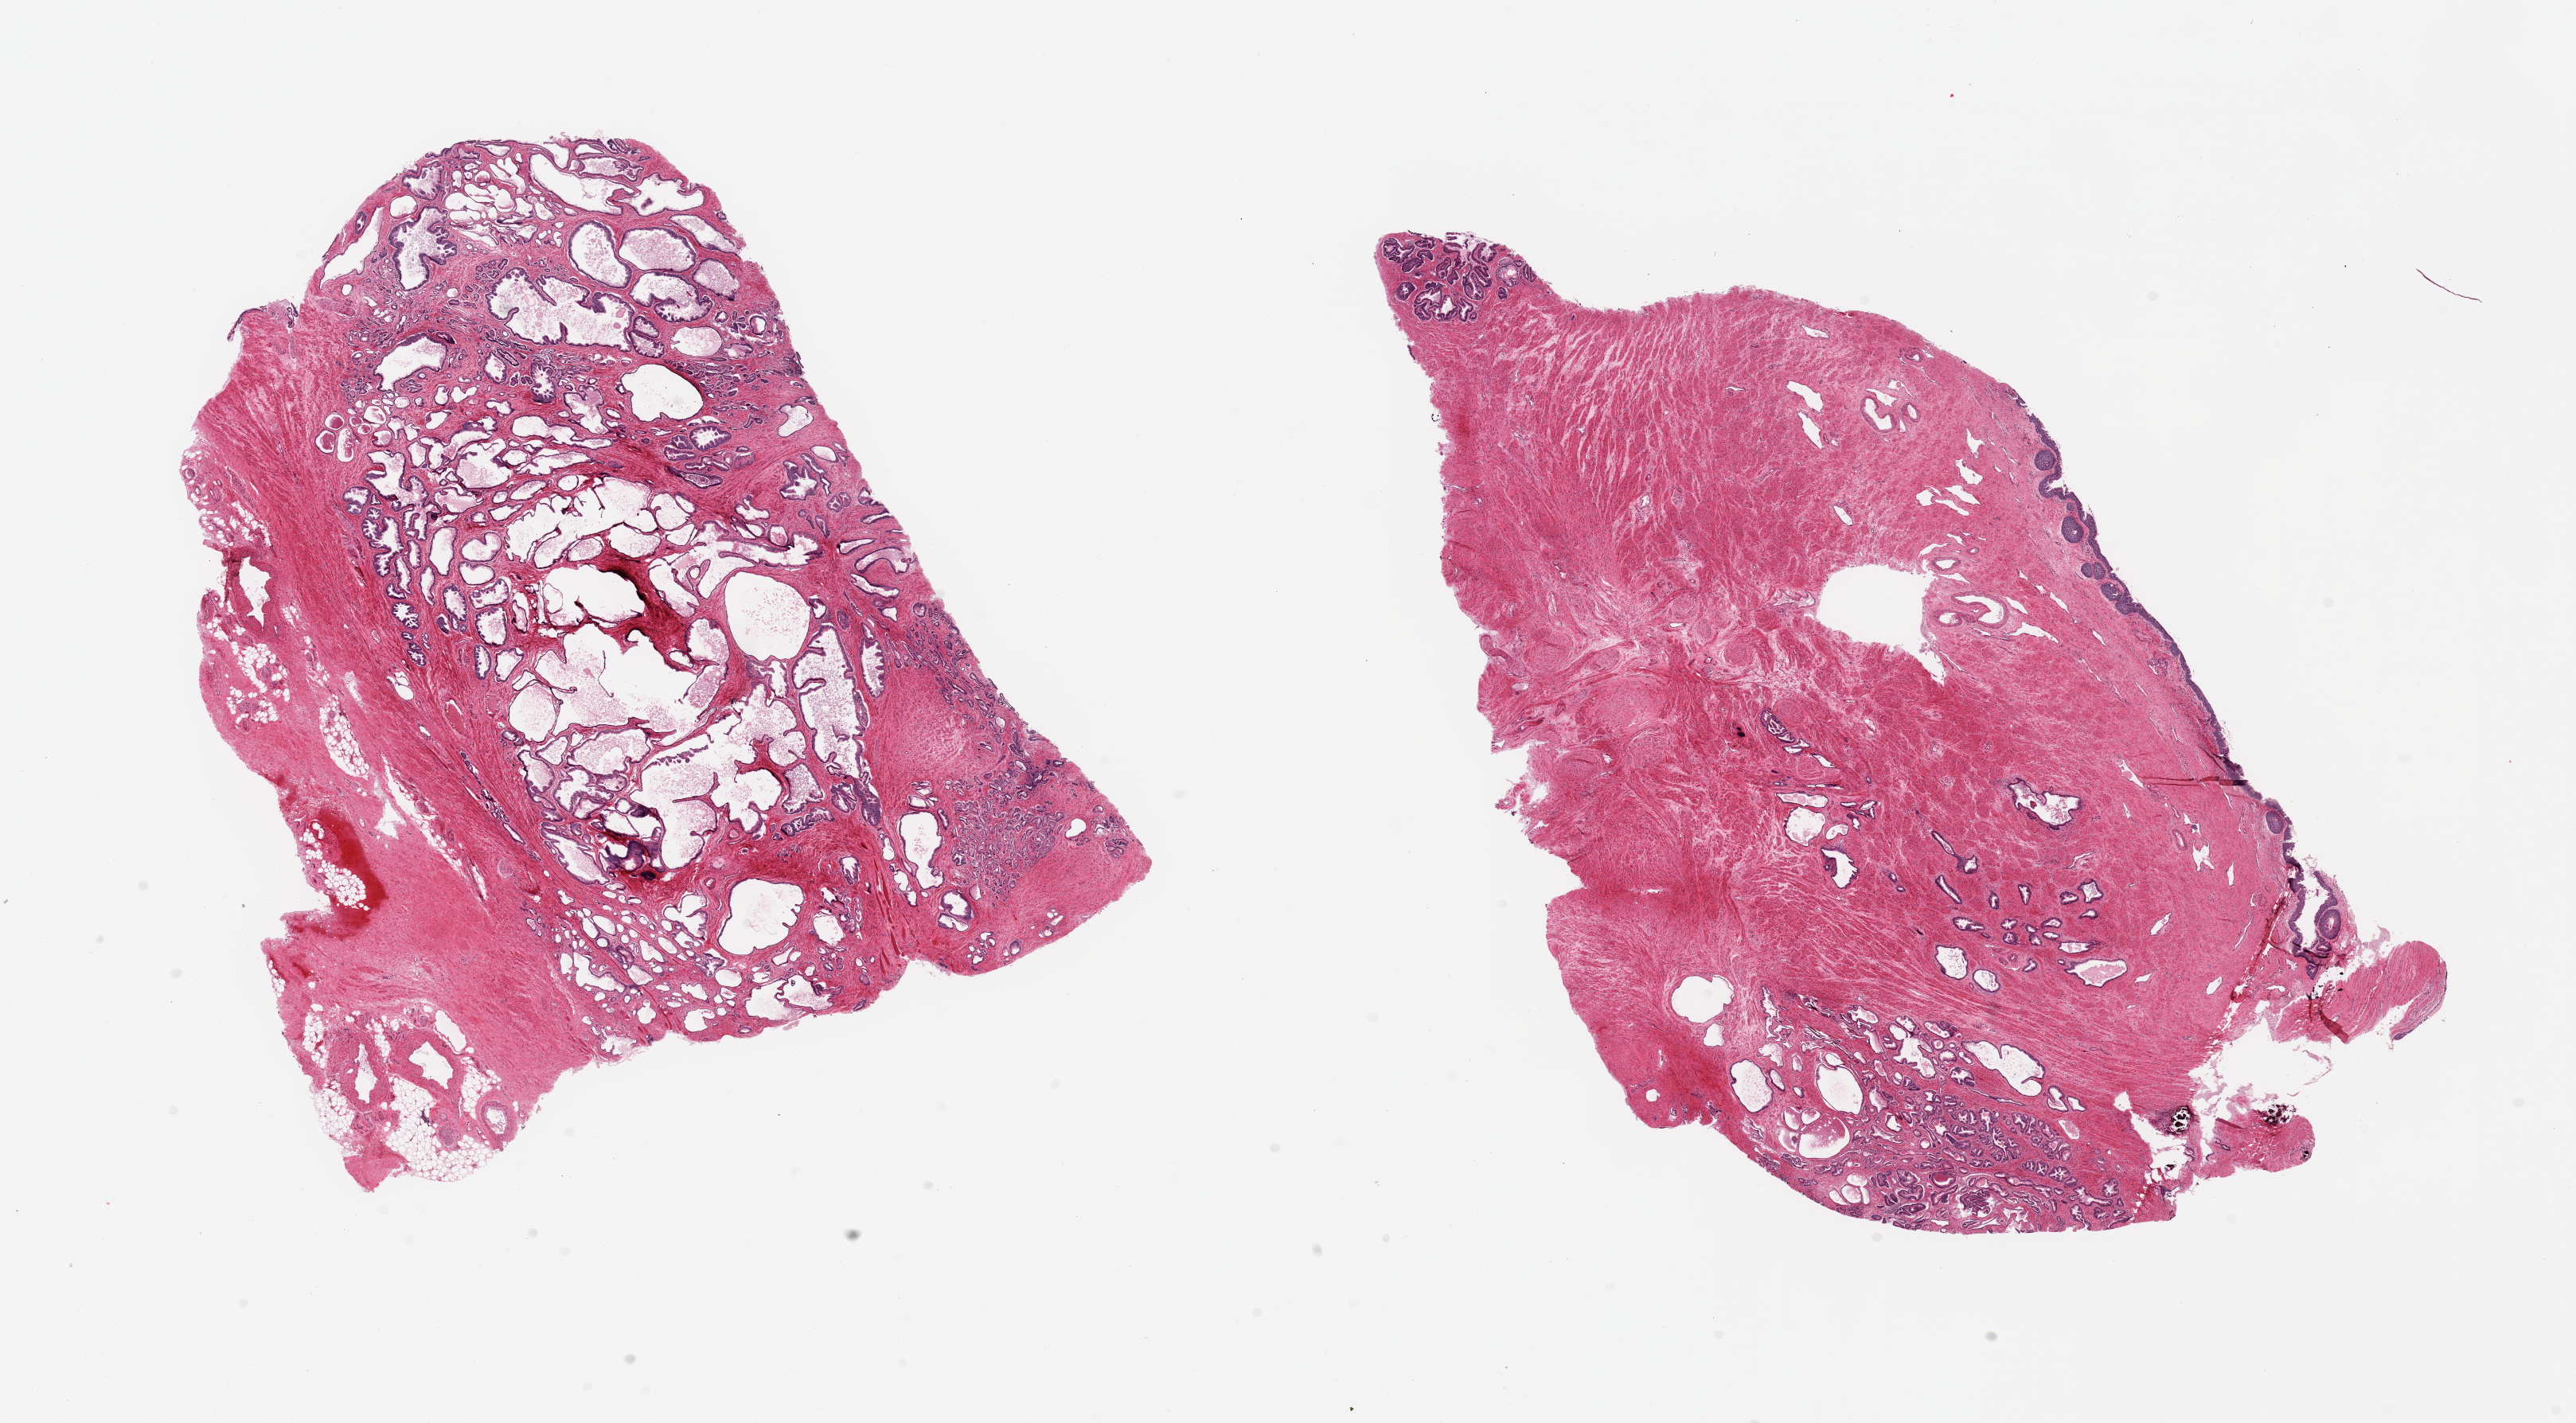
Whole-slide image, hematoxylin and eosin (H&E) stain — a low-resolution overview of the entire scanned area, about 25.6 x 14.1 mm; PAXgene-fixed, paraffin-embedded tissue; section of prostate (target tissue); donor tissue sample.
Review note (as recorded): 2 pieces, hyerplasia, several 1-2 mm microfoci of Adenocarcinoma, 3+3=6.